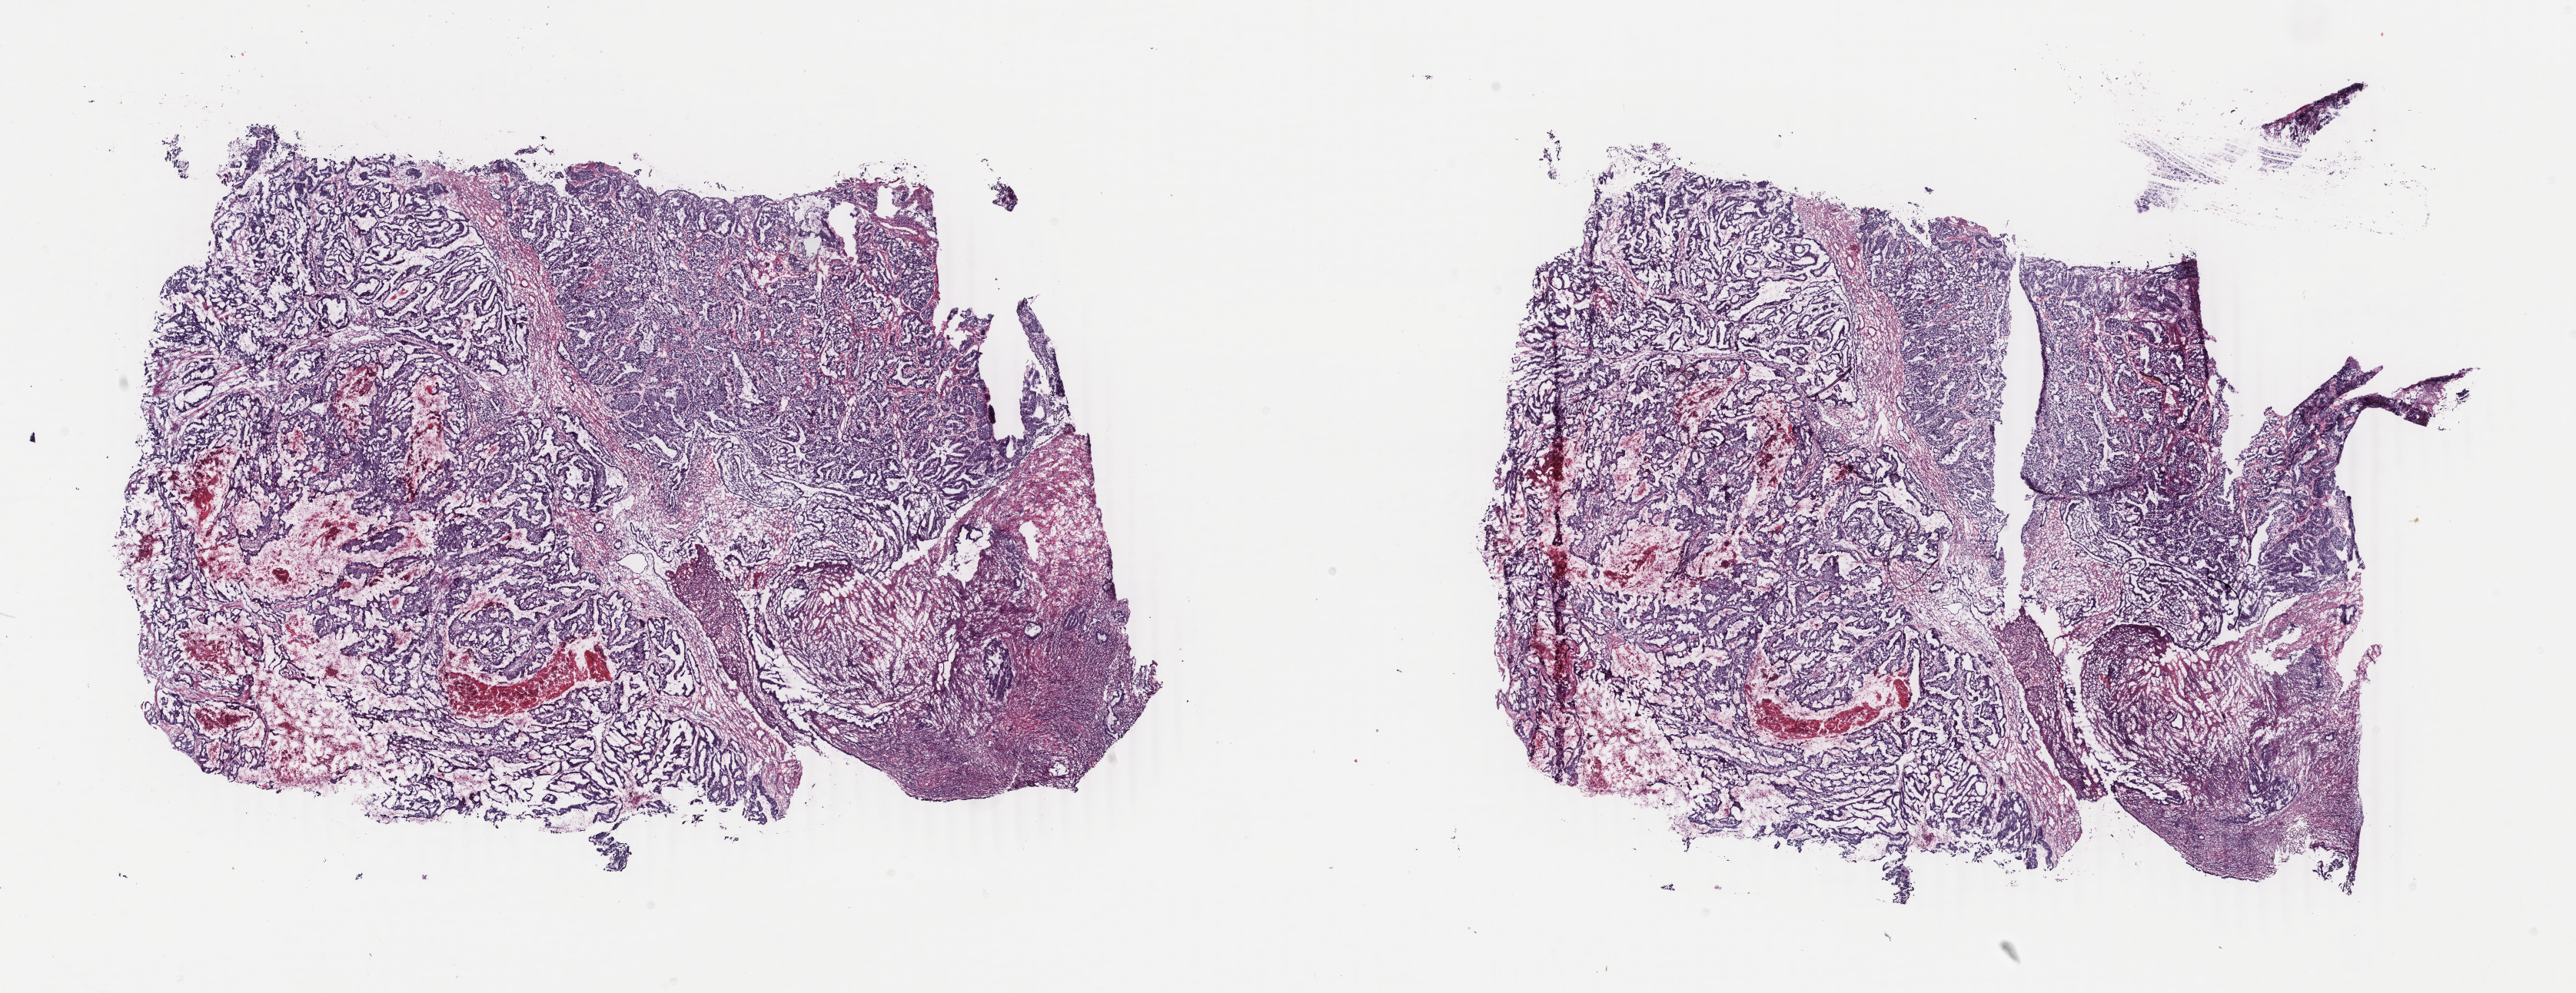
Whole-slide histology image, Hematoxylin and eosin (H&E) stained — whole scanned area (about 26.7 x 10.3 mm) shown as a low-resolution overview. Frozen section. Sample: primary tumour, uterus. Female, age 60 years at initial diagnosis. Histologic grade: G3 (poorly differentiated). Pathologist review of this section (percent, as recorded): tumour cells 60%, tumour nuclei 80%, normal cells 20%, stromal cells 0%, necrosis 20%. Infiltration values recorded for this section: lymphocyte infiltration 20%, monocyte infiltration 0%, neutrophil infiltration 20%.
• lymph nodes positive (case pathology): 0 of 6 examined
• histologic diagnosis: Endometrioid adenocarcinoma, NOS (endometrium)
• FIGO stage: IB